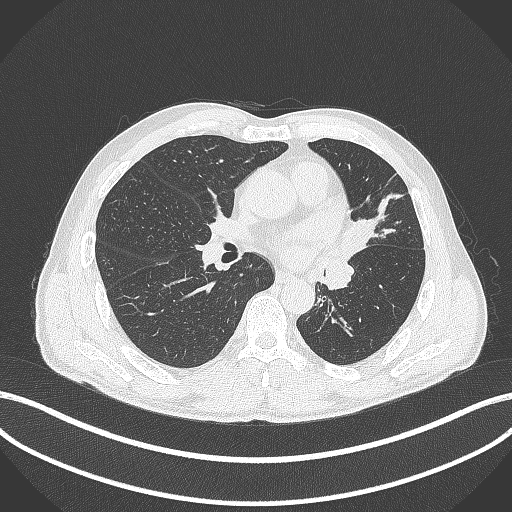
Chest CT, one axial slice. Position 222 of 429 along the scan axis. Lung window (W 1500 / L -600 HU). 1 mm slice thickness. 512 × 512 image matrix, field of view 400 × 400 mm. Patient: male, 57 years. Case-level facts recorded for this patient, not image findings: clinical TNM (as recorded): T2b N0 M0.
Outlined on this slice (rectangle marked by the reading radiologist):
- lung tumour (recorded histology: squamous cell carcinoma): box from (x=334, y=210) to (x=374, y=264) px